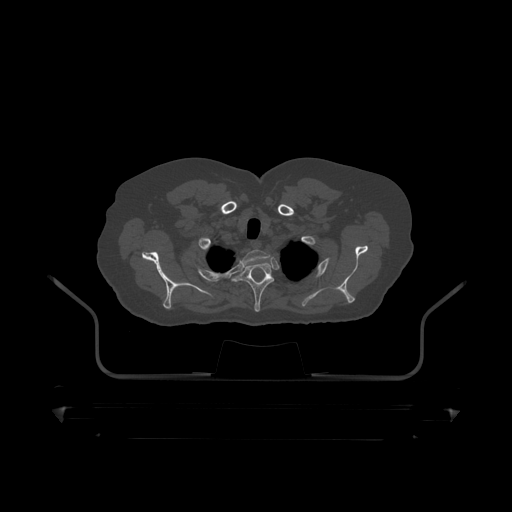
CT including the spine, one axial slice; slice 376 of 390 in the series (ordered by position); 120 kVp; bone window (W 1800 / L 400 HU); 1.25 mm slice thickness; 512 × 512 image matrix. Male patient, age 60 years. Case-level facts recorded for this patient, not image findings: primary cancer: prostate.
Outlined on this slice (semi-automatic segmentation, software-assisted and operator-edited):
- T1 vertebra: bounding box (x1, y1, x2, y2) in pixels: (240, 250, 270, 268)
- T2 vertebra: (235, 262, 275, 312)
- T3 vertebra: (265, 279, 284, 292)